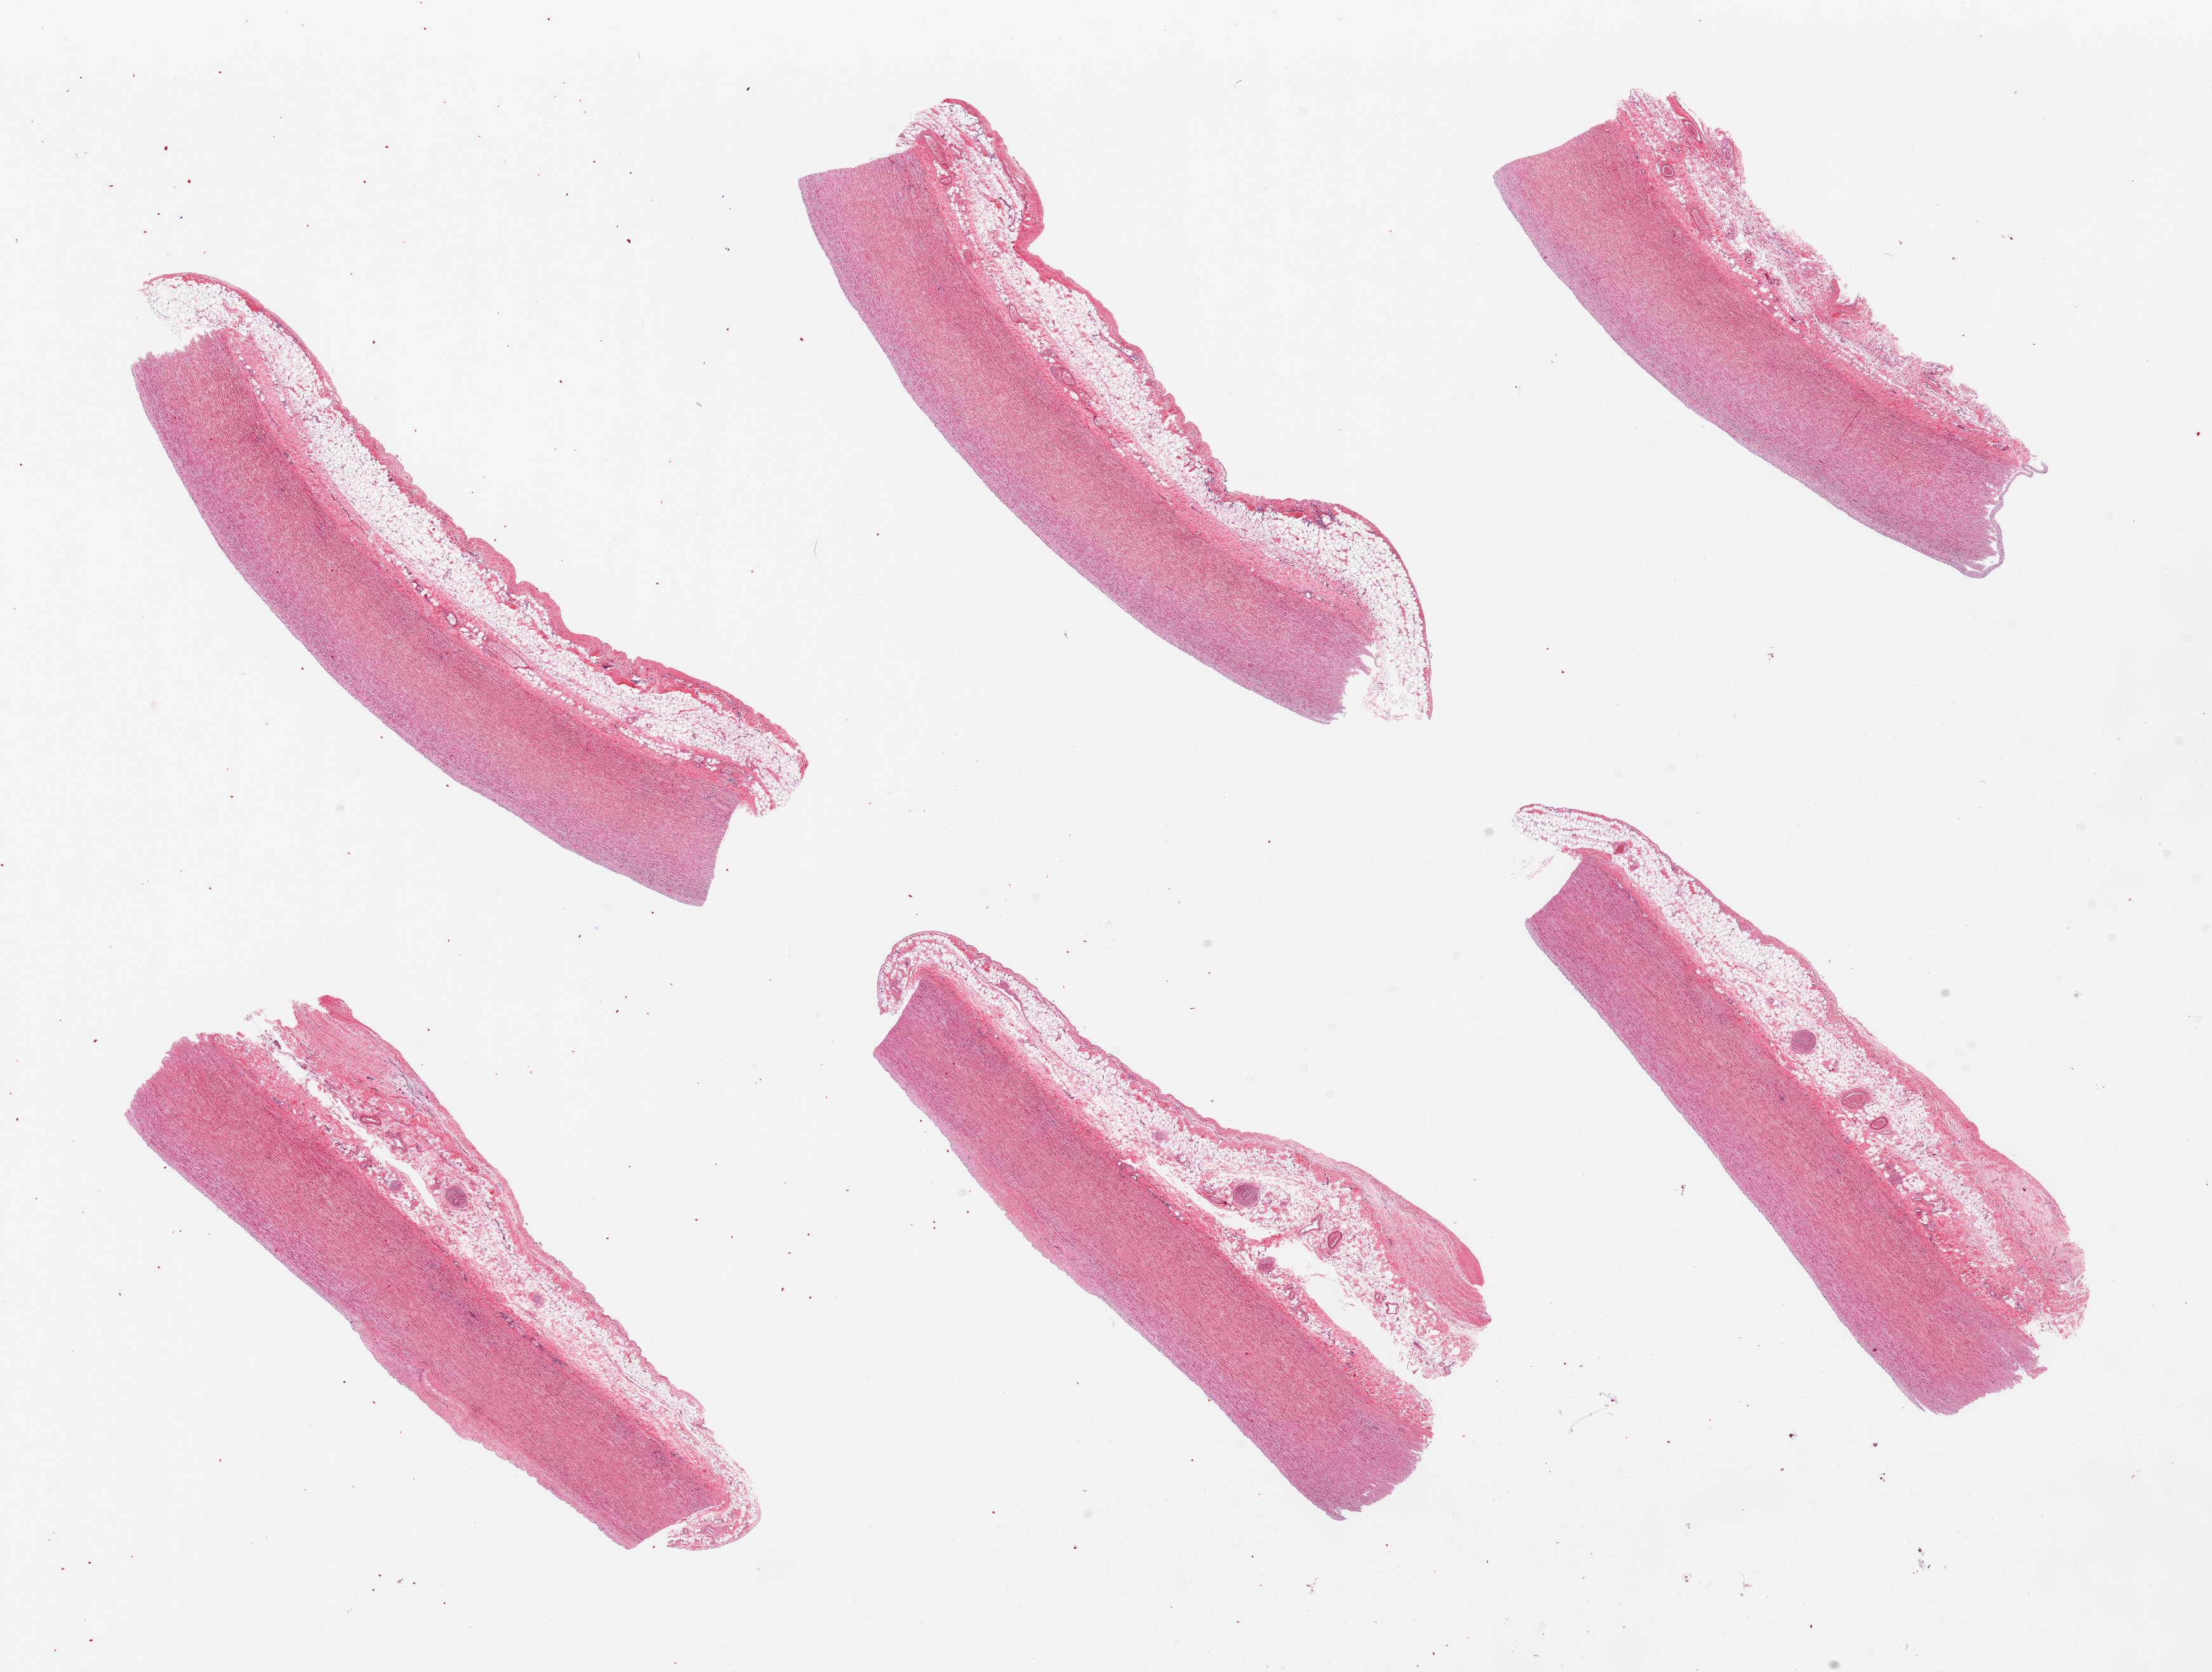
Whole-slide image, haematoxylin and eosin stain, brightfield, low-resolution overview of the scanned area, about 27.6 x 20.8 mm (slide scanned at 20x). PAXgene-fixed paraffin-embedded (PFPE) section. Sampled site (target tissue): aorta. Tissue donor sample. Female donor.
Pathologist's review note for this sample: 6 pieces, attached adventitia/fat, some intimal thickening.